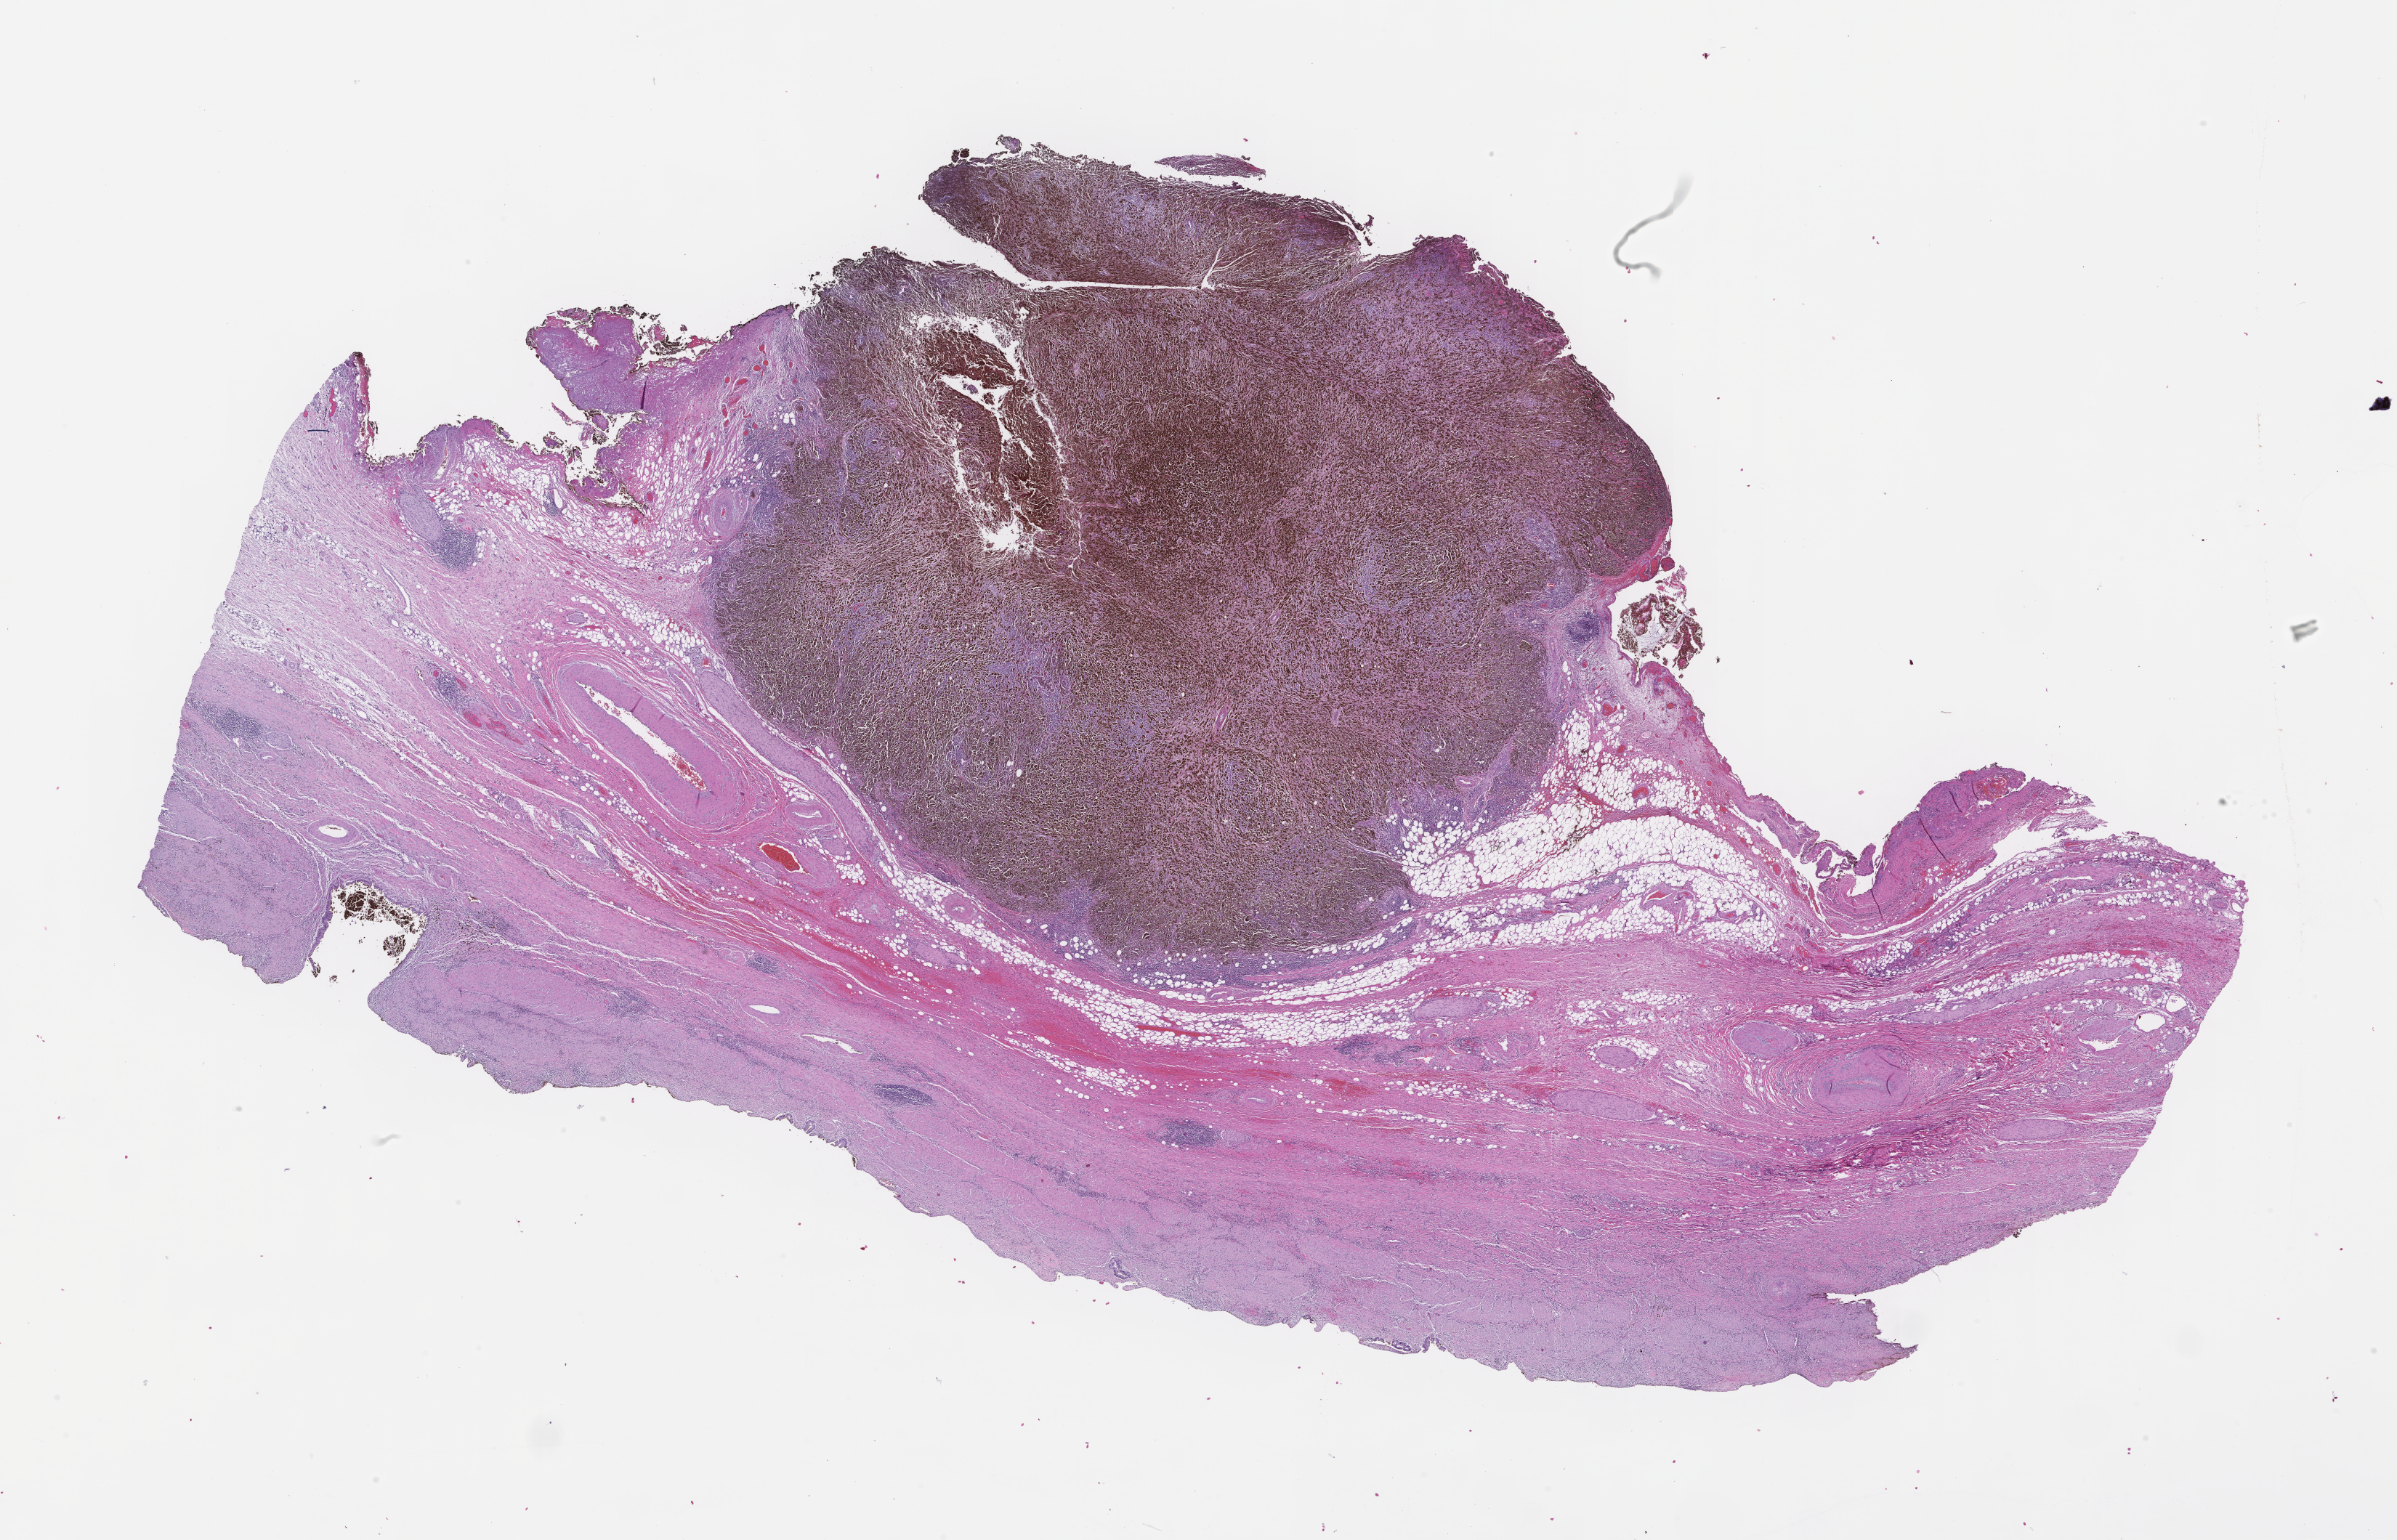
H&E whole-slide image — shown as a low-resolution overview of the whole scanned area (about 26.6 x 17.1 mm), formalin-fixed paraffin-embedded section, site: skin, archival tissue. Patient: female.
• this section: primary tumor
• diagnosis: Melanoma